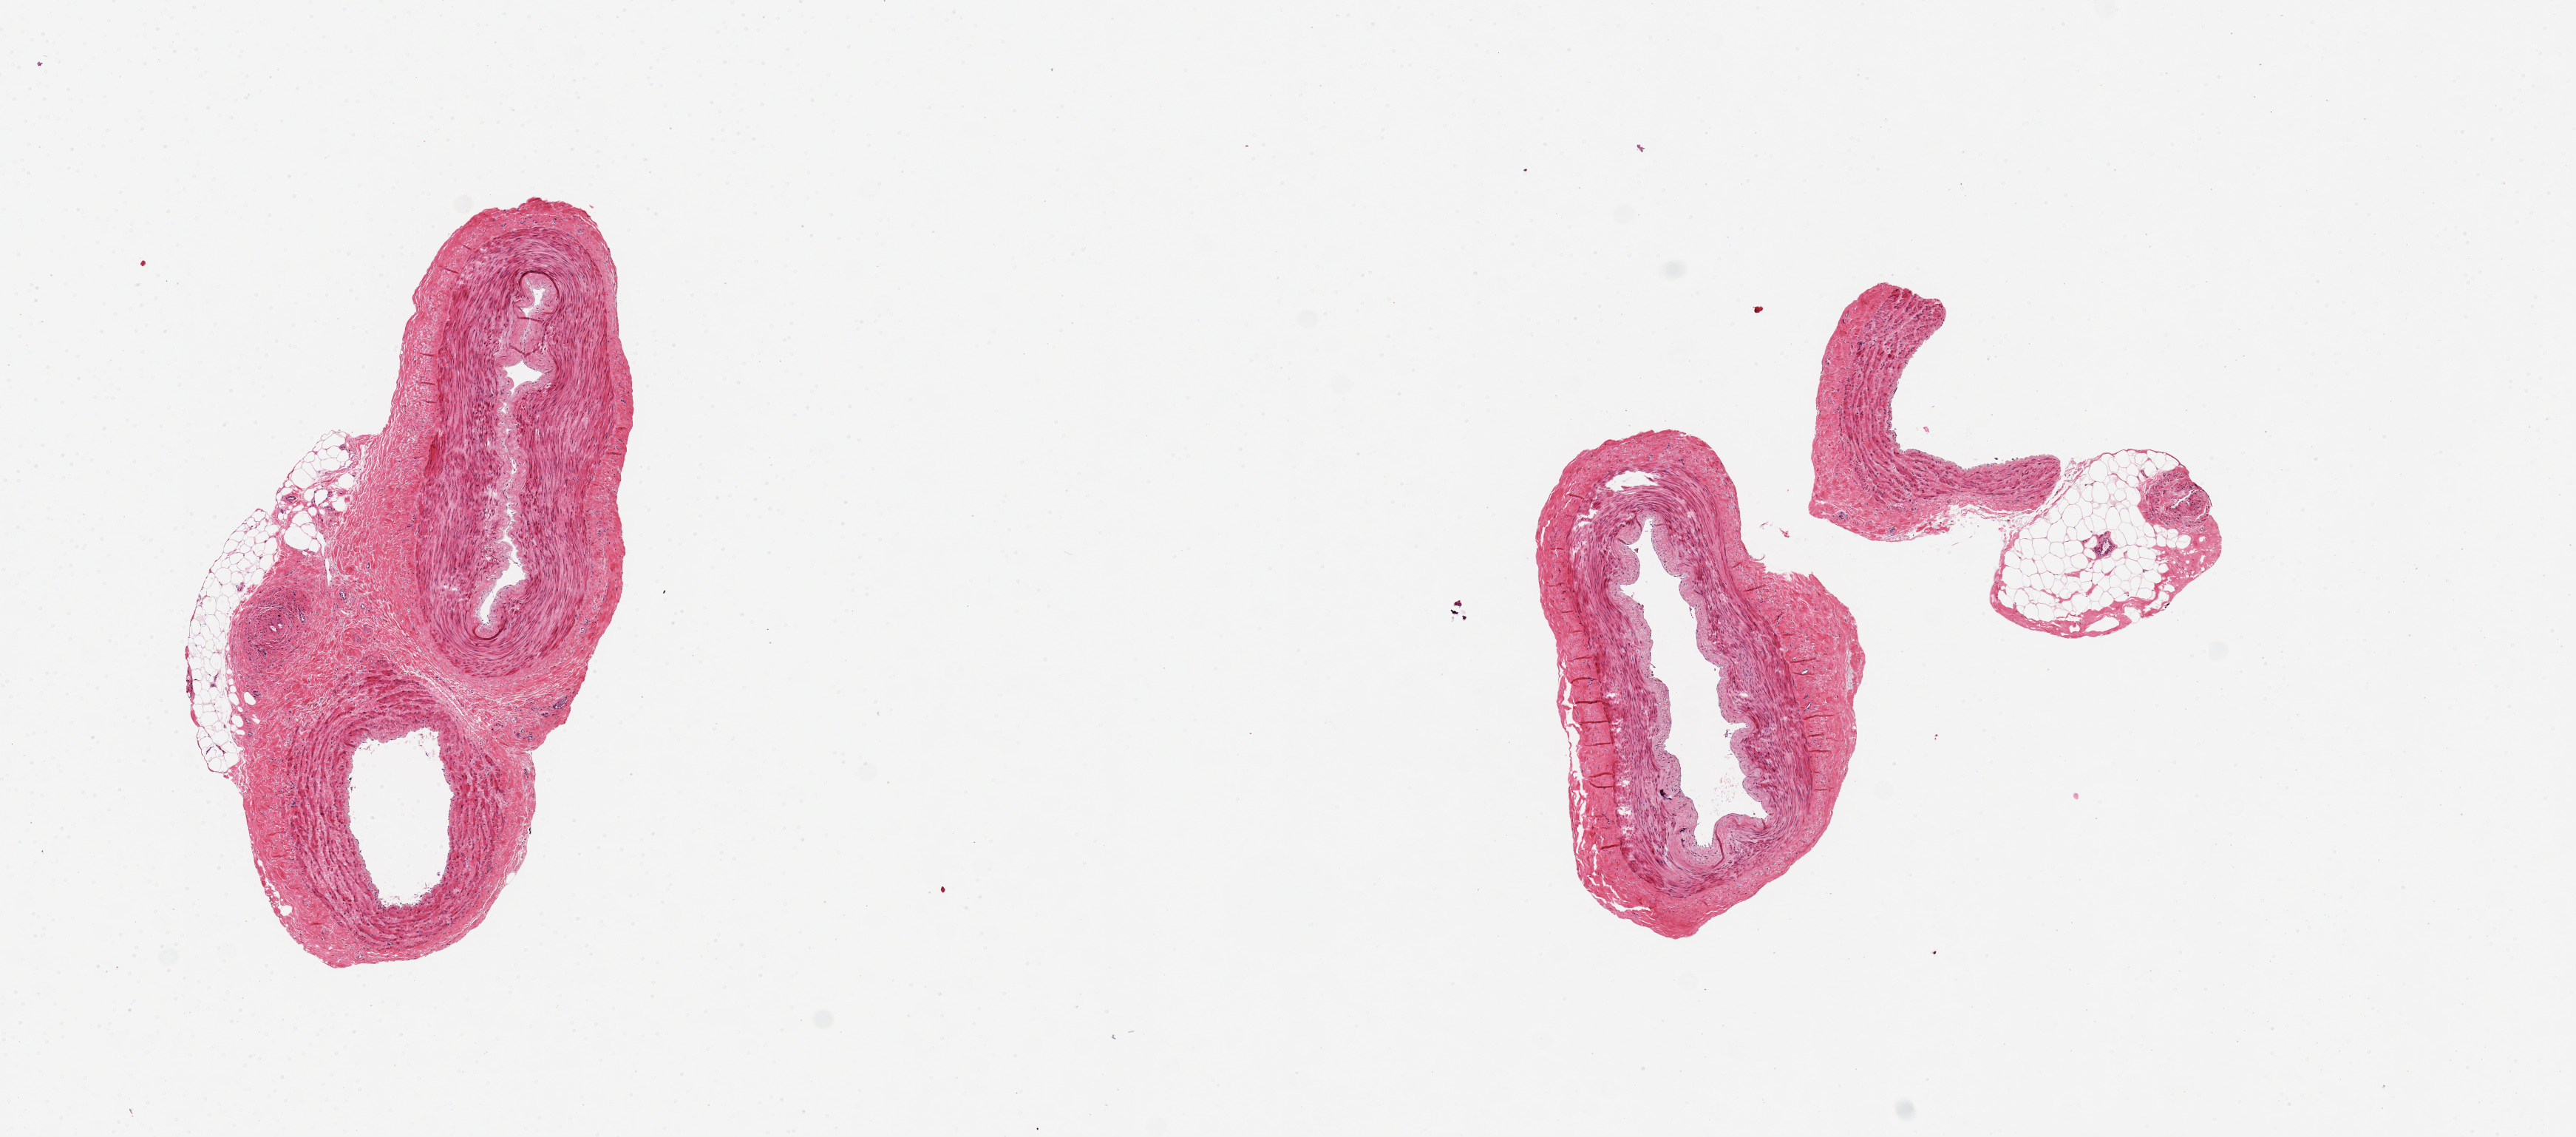
Digitized hematoxylin and eosin (H&E)-stained section, brightfield — low-resolution overview of the scanned area, about 13.8 x 6.1 mm; PAXgene-fixed paraffin-embedded (PFPE) section; sampled site (target tissue): tibial artery; tissue donor sample. Female donor.
• review note (as recorded): 2 pieces with additional minute fragments of fat/fibrous tissue (avoid); fairly clean specimens, one a section through a bifurcation in the artery